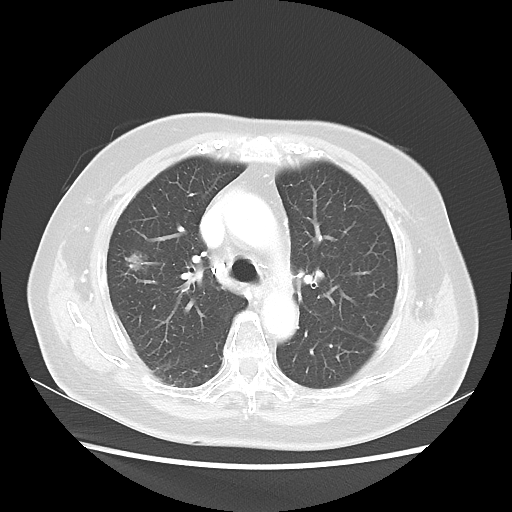
Chest CT, one axial slice. Slice 32 of 48 in the series (ordered by position). Reconstruction kernel LUNG. 100 kVp. Lung window (W 1500 / L -600 HU). 512 × 512 image matrix, field of view 360 × 360 mm. Female patient, age 75 years. From the clinical record (not read from this slice): clinical TNM (as recorded): T1c N0 M0.
Outlined on this slice (bounding box drawn by a radiologist):
- lung tumour (recorded histology: adenocarcinoma): bounding box <125,248,151,280> (left, top, right, bottom; pixels)